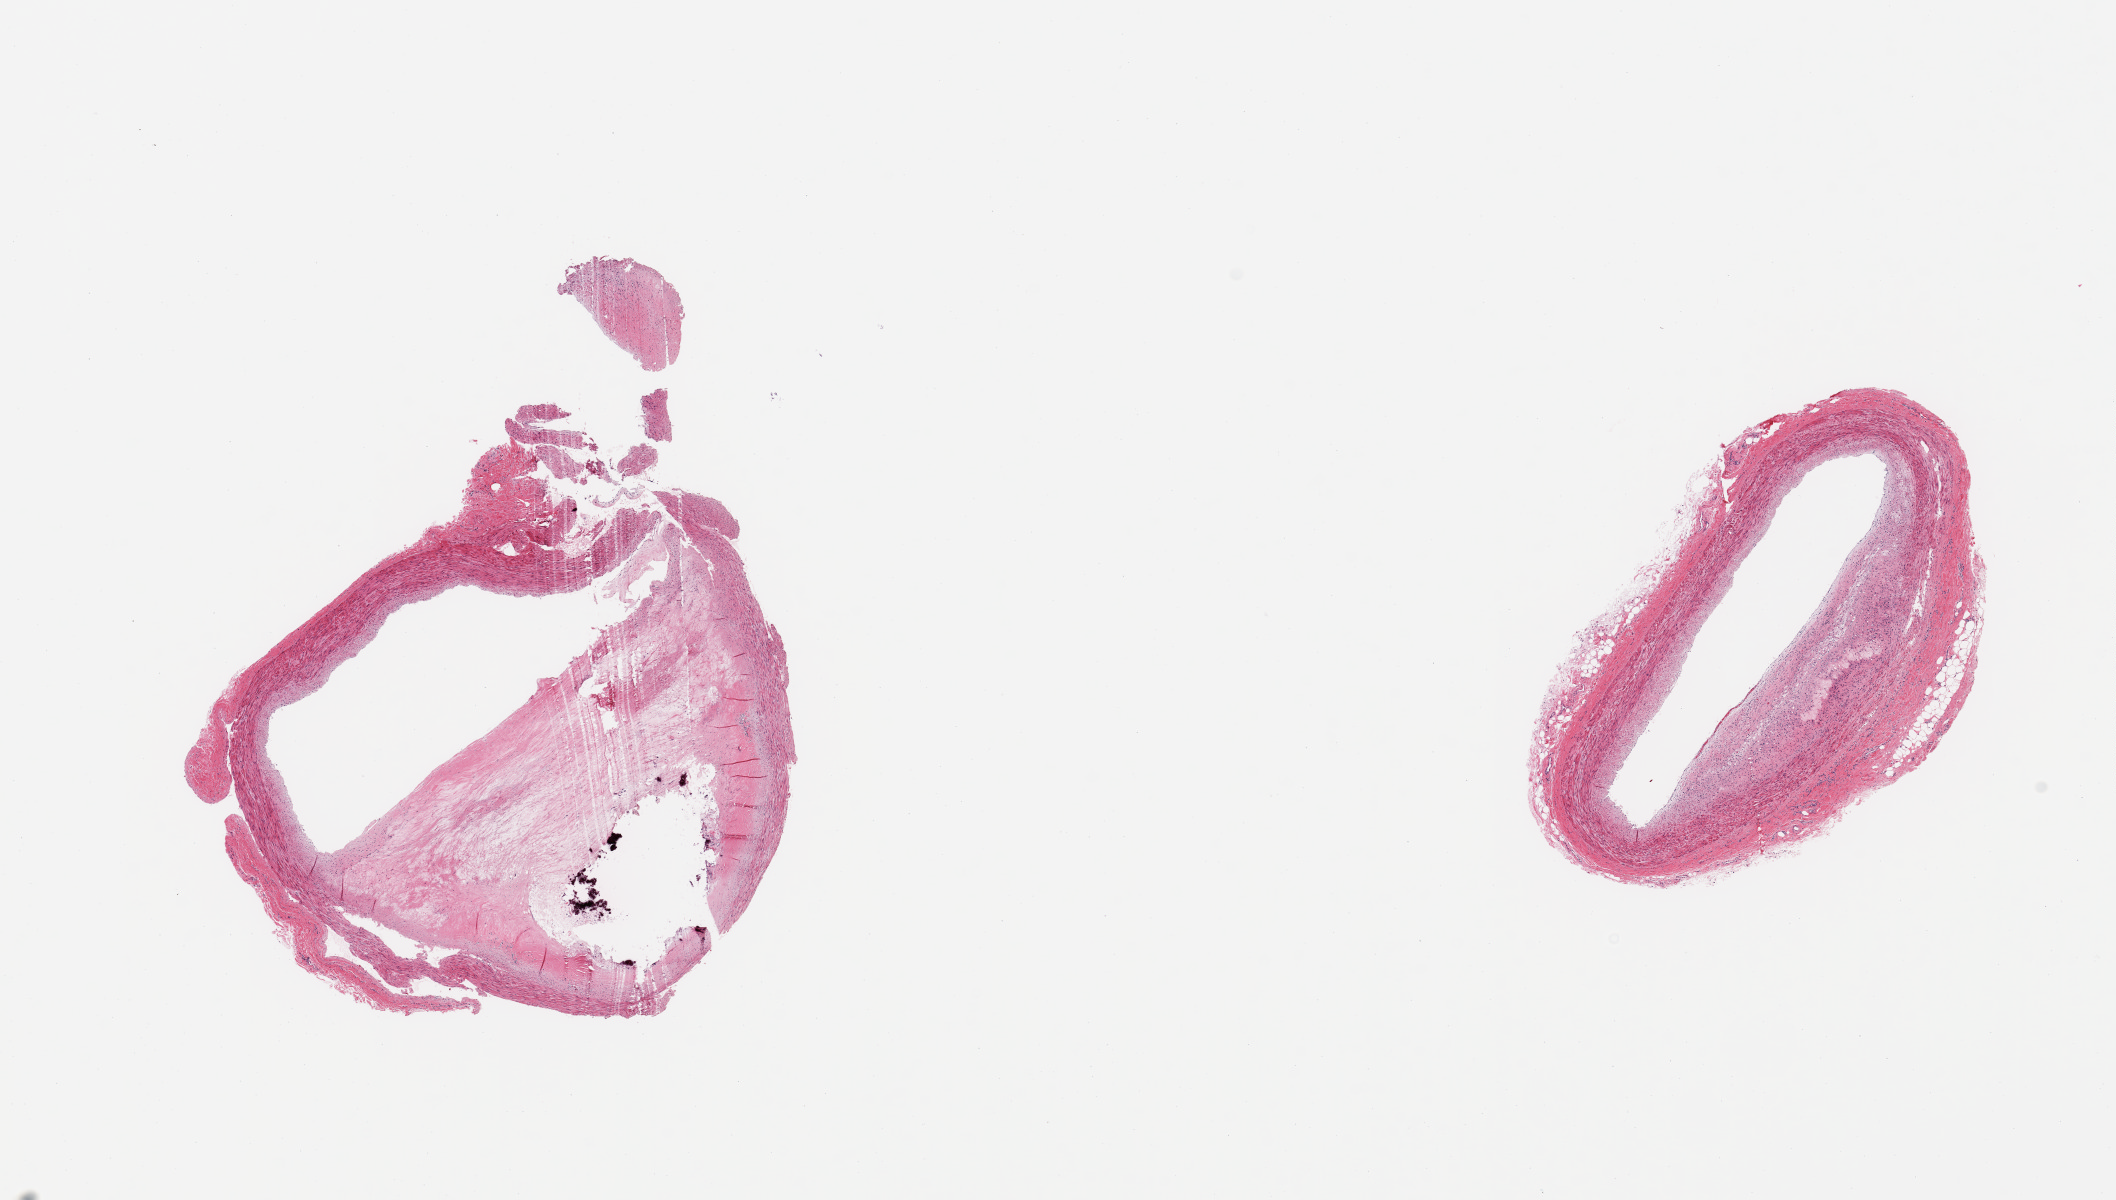
Whole-slide image, hematoxylin and eosin (H&E) stain, a low-resolution overview of the entire scanned area, about 16.7 x 9.5 mm (acquisition: 20x scan); PAXgene-fixed, paraffin-embedded tissue; sampled site (target tissue): coronary artery; tissue donor sample. Donor: male.
Pathologist's review note for this sample: 2 pieces; eccentric fibrosclerotic plaque with calcification and with narrowing of the lumen by 60%; narrow rim of adventitia and fat.